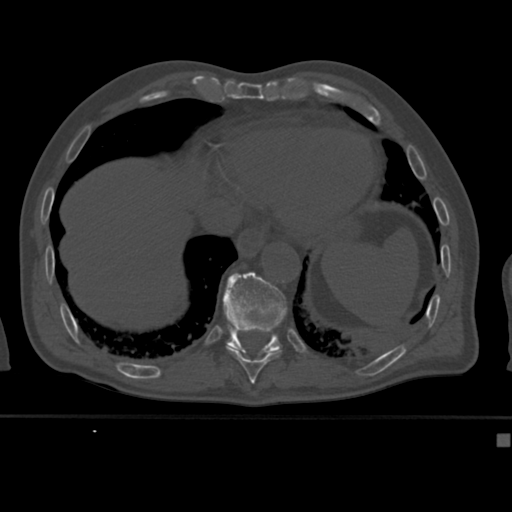
CT including the spine, one axial slice; slice 221 of 430 in the series (ordered by position); reconstruction kernel Br40s; bone window (W 1800 / L 400 HU); 1.5 mm slice thickness; 512 × 512 image matrix, field of view 337 × 337 mm. Male patient, age 64 years. From the clinical record (not read from this slice): primary cancer: uterus.
Outlined on this slice (semi-automatically segmented with operator editing):
- T10 vertebra: bounding box (x1, y1, x2, y2) in pixels: (227, 347, 281, 382)
- T11 vertebra: (223, 271, 287, 356)